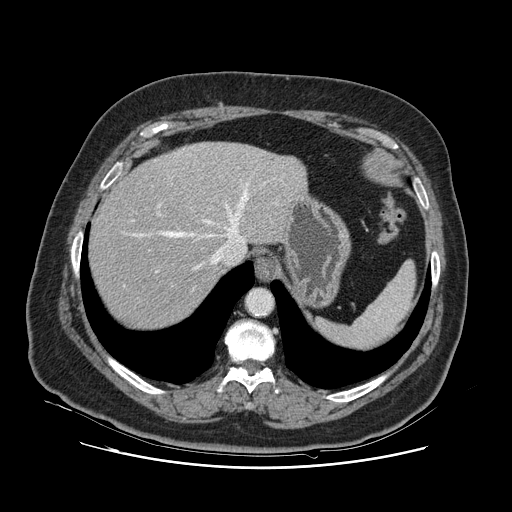
Contrast-enhanced abdominal CT, one axial slice; position 98 of 132 along the scan axis; 120 kVp; intravenous contrast given; soft-tissue window (W 400 / L 40 HU); 512 × 512 image matrix, field of view 391 × 391 mm. Female patient, age 73 years. From the clinical record (not read from this slice): diagnosis: colorectal cancer liver metastases, imaged before liver resection; multiple liver metastases: no; largest metastasis: 7 cm; disease in both lobes: no.
Outlined on this slice (expert manual segmentation):
- hepatic veins: box from (x=123, y=177) to (x=249, y=287) px
- liver: (x=90, y=143)–(x=305, y=330)
- planned liver remnant (the part of the liver to remain after resection): (x=90, y=161)–(x=228, y=330)
- portal vein (with intrahepatic branches): (x=155, y=203)–(x=161, y=273)